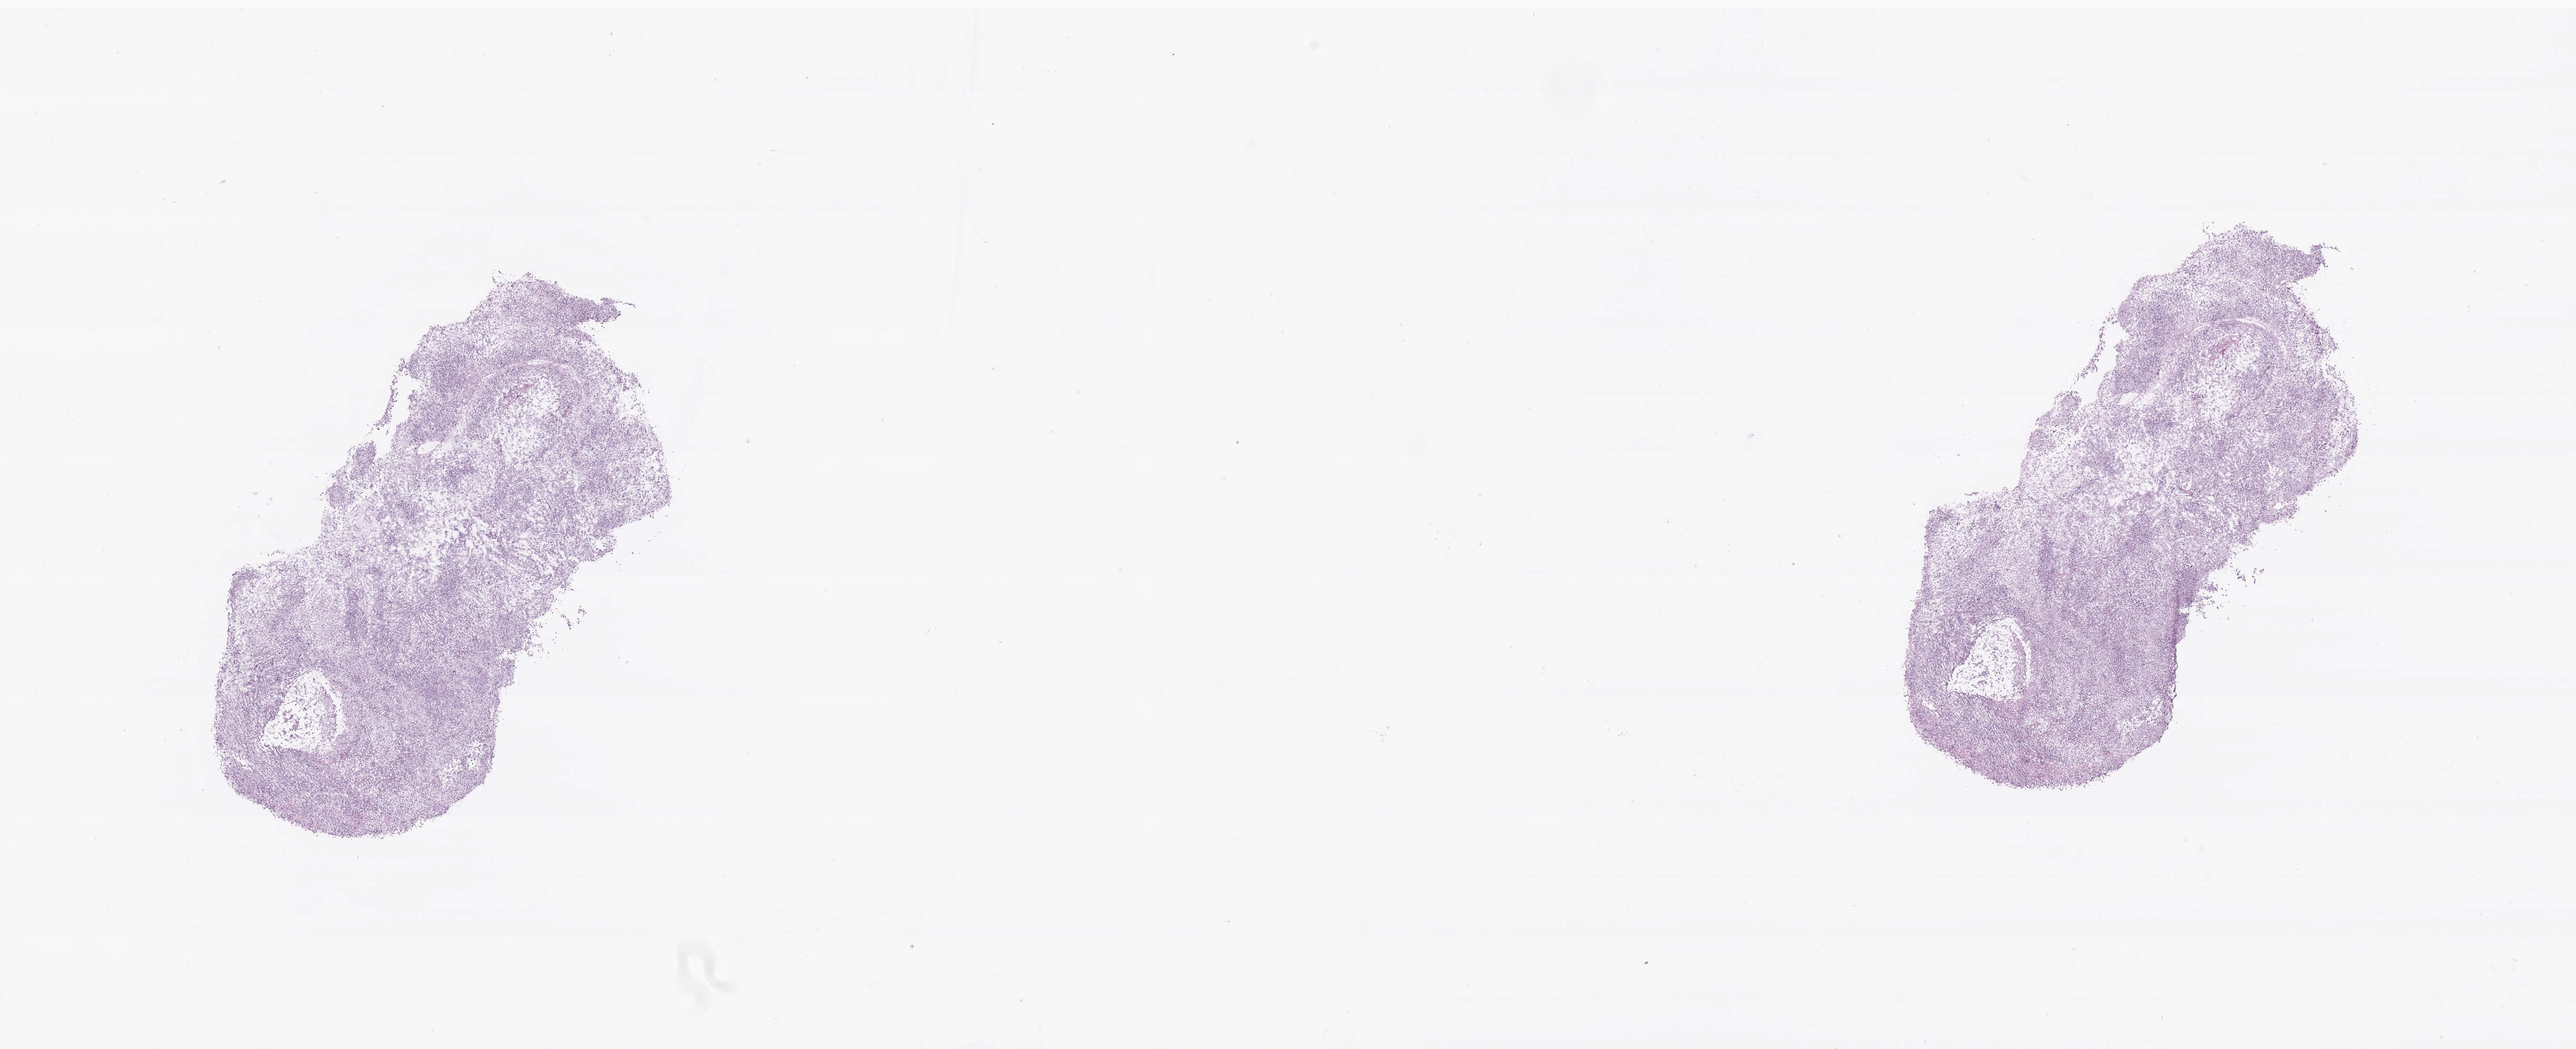
Digitized H&E-stained section of tumor tissue from the brain, shown as a low-resolution overview of the whole scanned area (about 22.8 x 9.3 mm); frozen section. Patient male; age 104 months (8 years 8 months).
• recorded diagnosis: Medulloblastoma, NOS